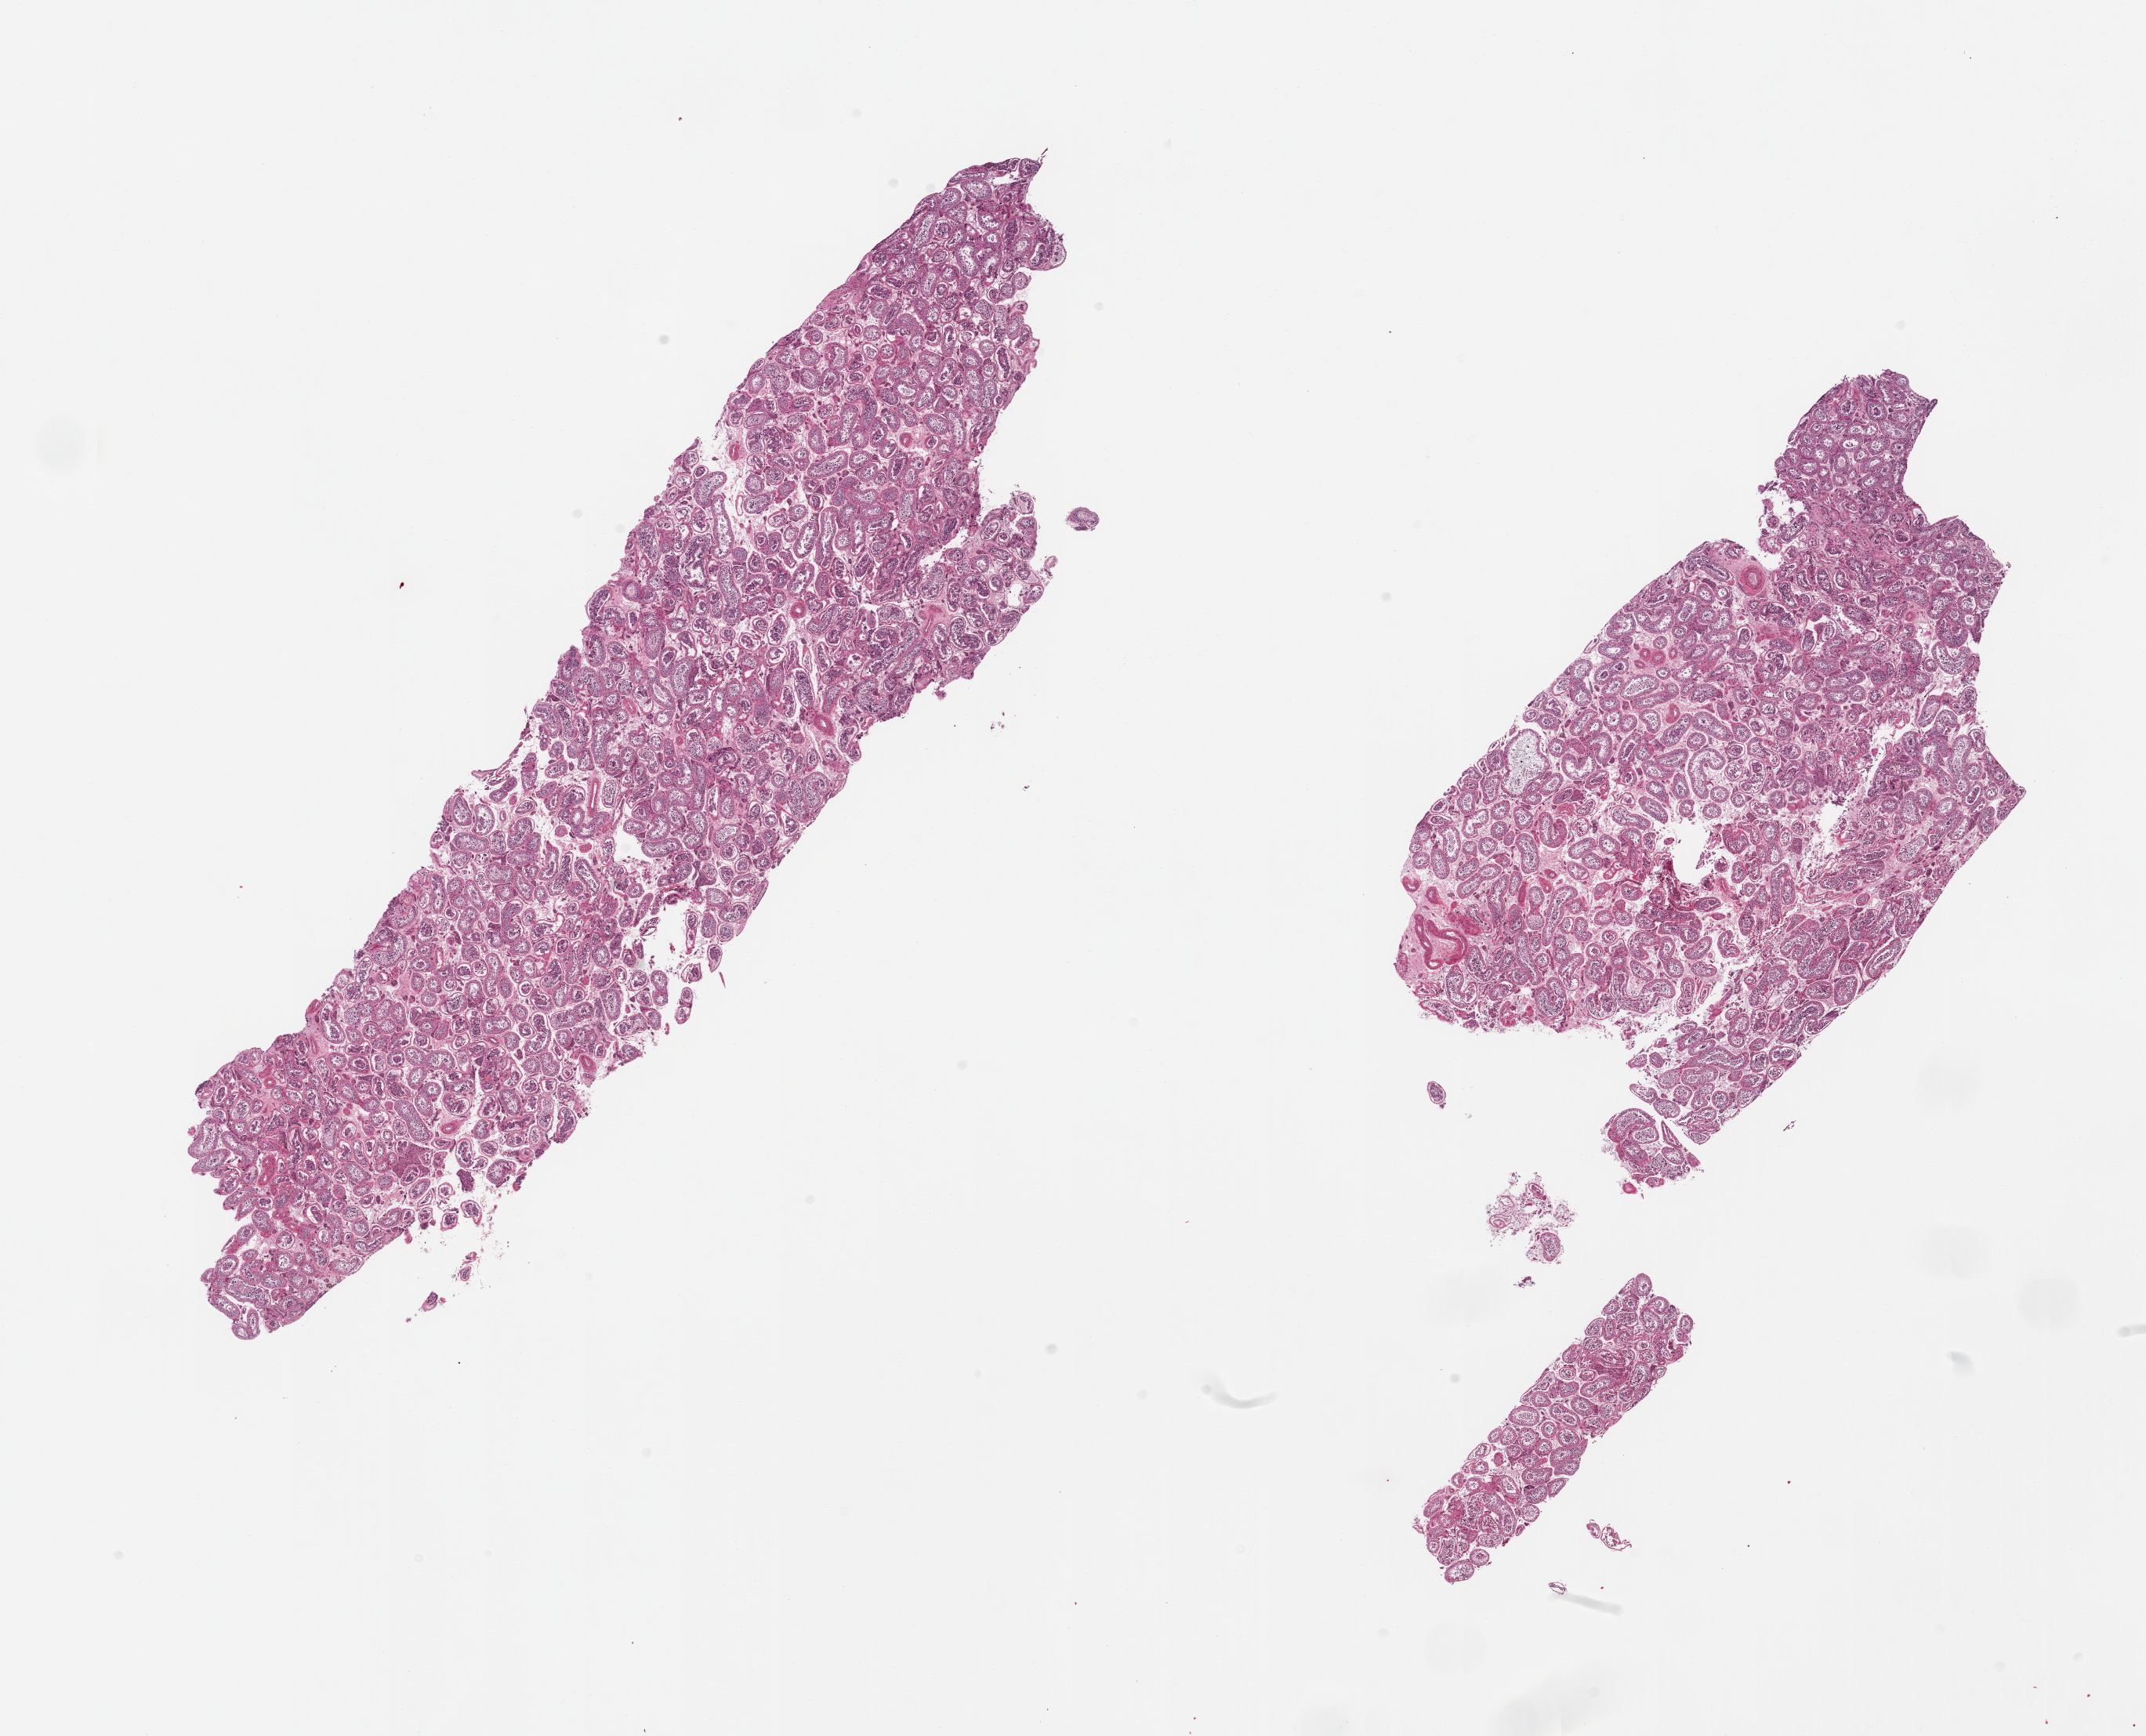
Haematoxylin and eosin whole-slide image — shown as a low-resolution overview of the whole scanned area (about 21.7 x 17.5 mm, from a 20x scan). PAXgene-fixed, paraffin-embedded tissue. Target tissue: testis. Donor tissue sample.
Pathologist's review note for this sample: 2 pieces; spermatogenesis observed.